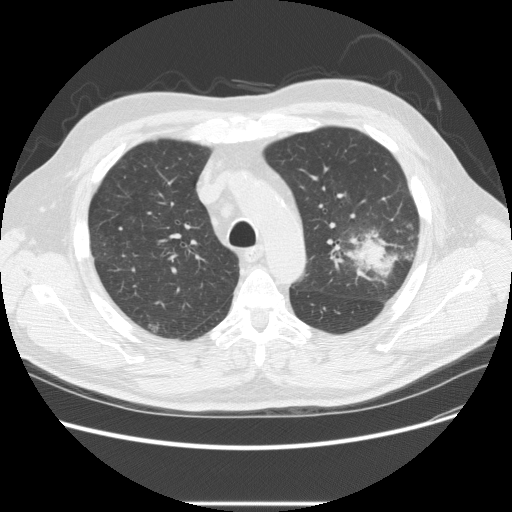
Chest CT (low-dose screening protocol), one axial image. Baseline screening round. Lung window (W 1500 / L -600 HU). 2.5 mm slice thickness. Standard (soft-tissue) reconstruction kernel (STANDARD). Slice 67 of 233 in the series. Male, age 73 years at enrolment.
Expert reader's lesion annotation, bounding box [x1, y1, x2, y2] px = [332, 215, 418, 287]. The screening reader recorded 2 non-calcified nodules or masses ≥4 mm on this exam; which of them this box marks is not recorded. Participant outcome: lung cancer diagnosed 11 days after this screen — bronchiolo-alveolar adenocarcinoma, NOS, other location, well differentiated (G1), stage IV (AJCC 6th edition).